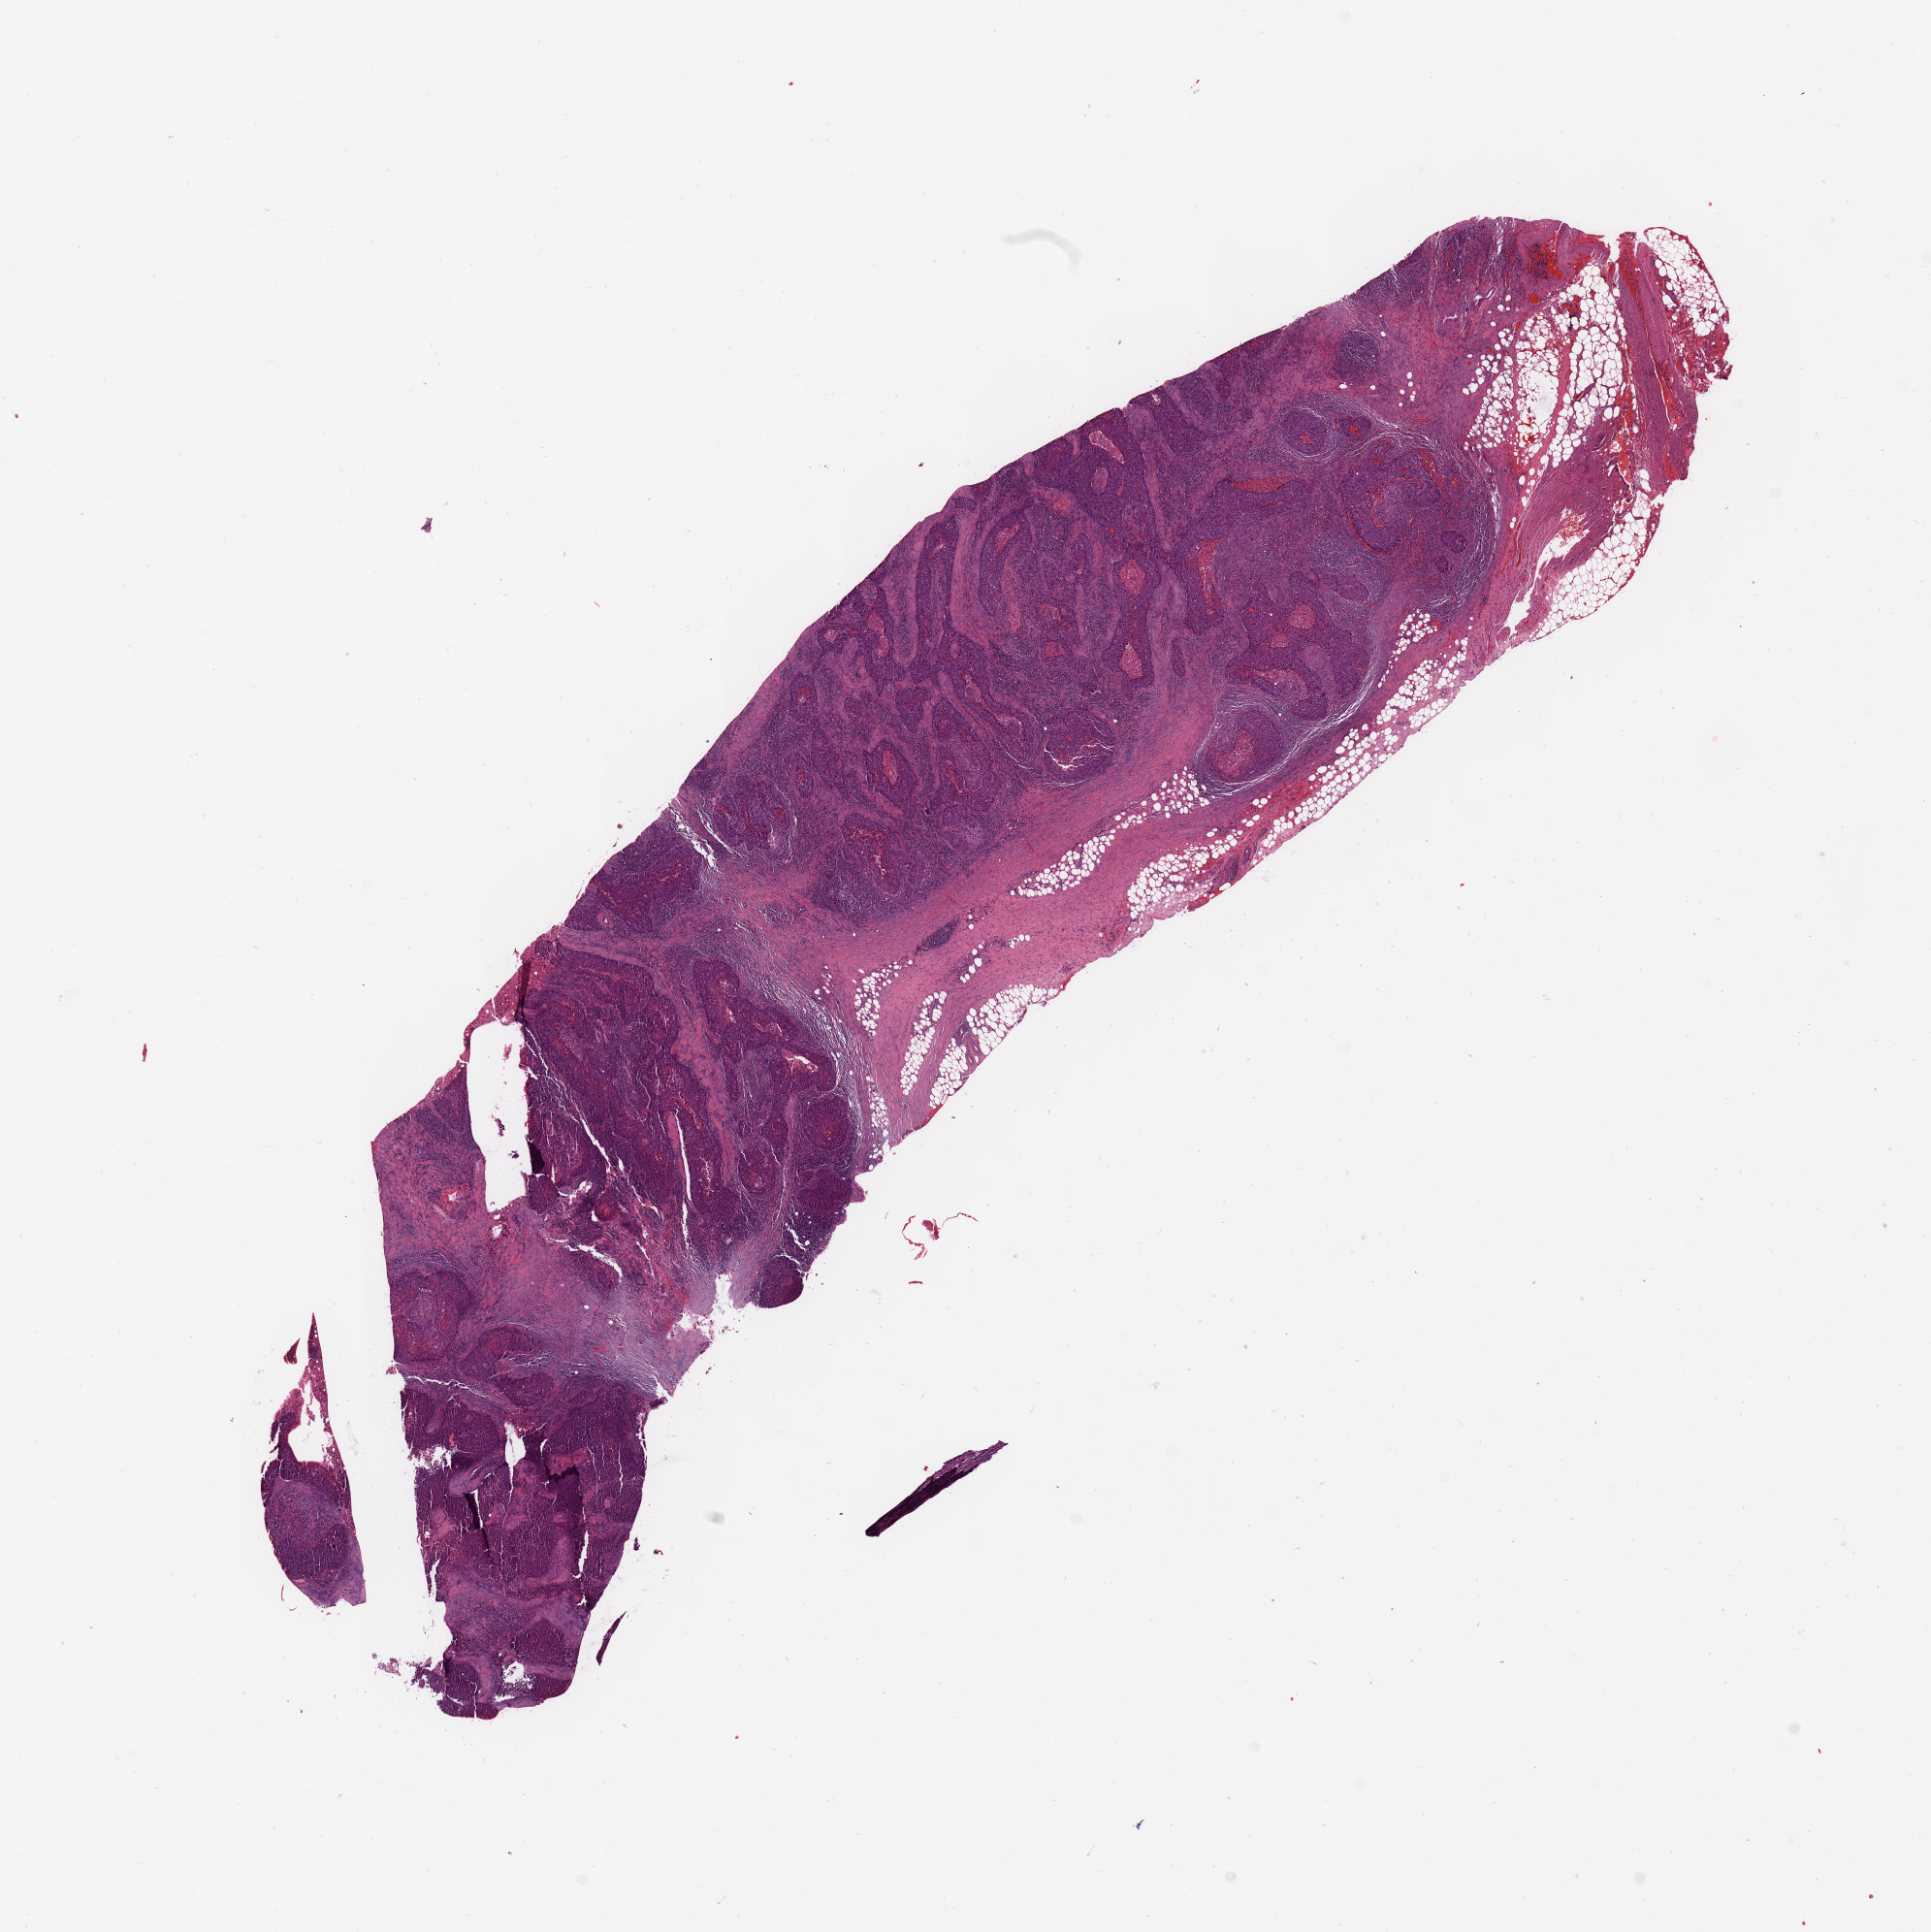
Digitized H&E tissue section (whole slide), shown as a low-resolution overview of the whole scanned area (about 15.8 x 15.8 mm); lung, tumour tissue. Male, 67 y/o. Histologic grade: G2 (moderately differentiated).
• diagnosis: Squamous cell carcinoma, NOS
• AJCC pathologic stage: IIIA